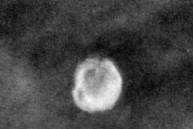
Region of interest cut from a scanned film mammogram (one marked finding); right breast; CC view.
Calcifications, morphology round and regular / eggshell; BI-RADS assessment category 2; benign without callback (not worked up further).